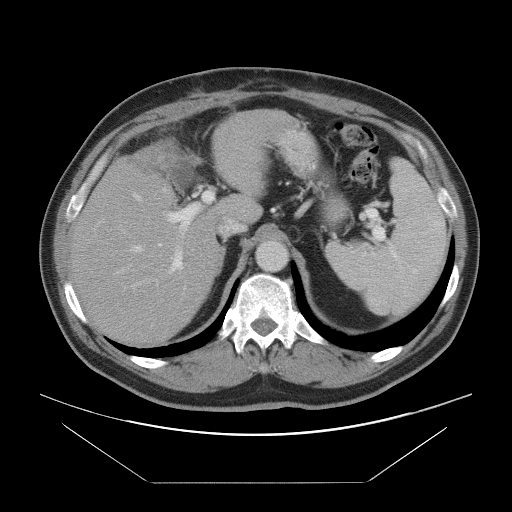
Contrast-enhanced abdominal CT, one axial slice. Slice 61 of 97 in the series (ordered by position). 120 kVp. Intravenous contrast given. Soft-tissue window (W 400 / L 40 HU). 5 mm slice thickness. 512 × 512 image matrix. Male patient, age 62 years. From the clinical record (not read from this slice): diagnosis: colorectal cancer liver metastases, imaged before liver resection.
Outlined on this slice (outlined manually by an expert reader):
- hepatic veins: bounding box (x1, y1, x2, y2) in pixels: (119, 187, 246, 272)
- liver: (73, 111, 289, 345)
- planned liver remnant (the part of the liver to remain after resection): (73, 174, 230, 345)
- portal vein (with intrahepatic branches): (101, 191, 214, 289)
- liver metastasis: (130, 149, 163, 177)